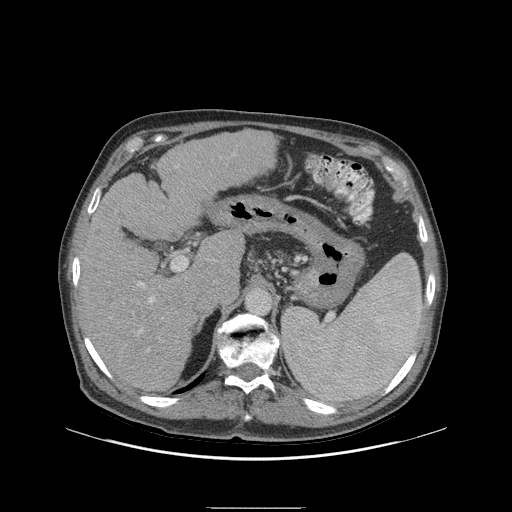
Contrast-enhanced abdominal CT (liver protocol), one axial slice. Position 59 of 105 along the scan axis. Reconstruction kernel STANDARD. 140 kVp. Soft-tissue window (W 400 / L 40 HU). 2.5 mm slice thickness. 512 × 512 image matrix, field of view 440 × 440 mm. Case-level facts recorded for this patient, not image findings: diagnosis: hepatocellular carcinoma (patient treated with transarterial chemoembolisation; whether this scan precedes or follows treatment is not stated here); TNM stage (as recorded): Stage-I; Child-Pugh class: A; tumour nodularity: uninodular; tumour size: 5.1 cm.
Structures marked on this image (semi-automatically segmented with operator editing):
- liver parenchyma outside the tumour (the mass and vessels are separate outlines, so this box may not span the whole liver): bounding box (x1, y1, x2, y2) in pixels: (78, 140, 243, 390)
- liver vessels: (138, 282, 155, 350)